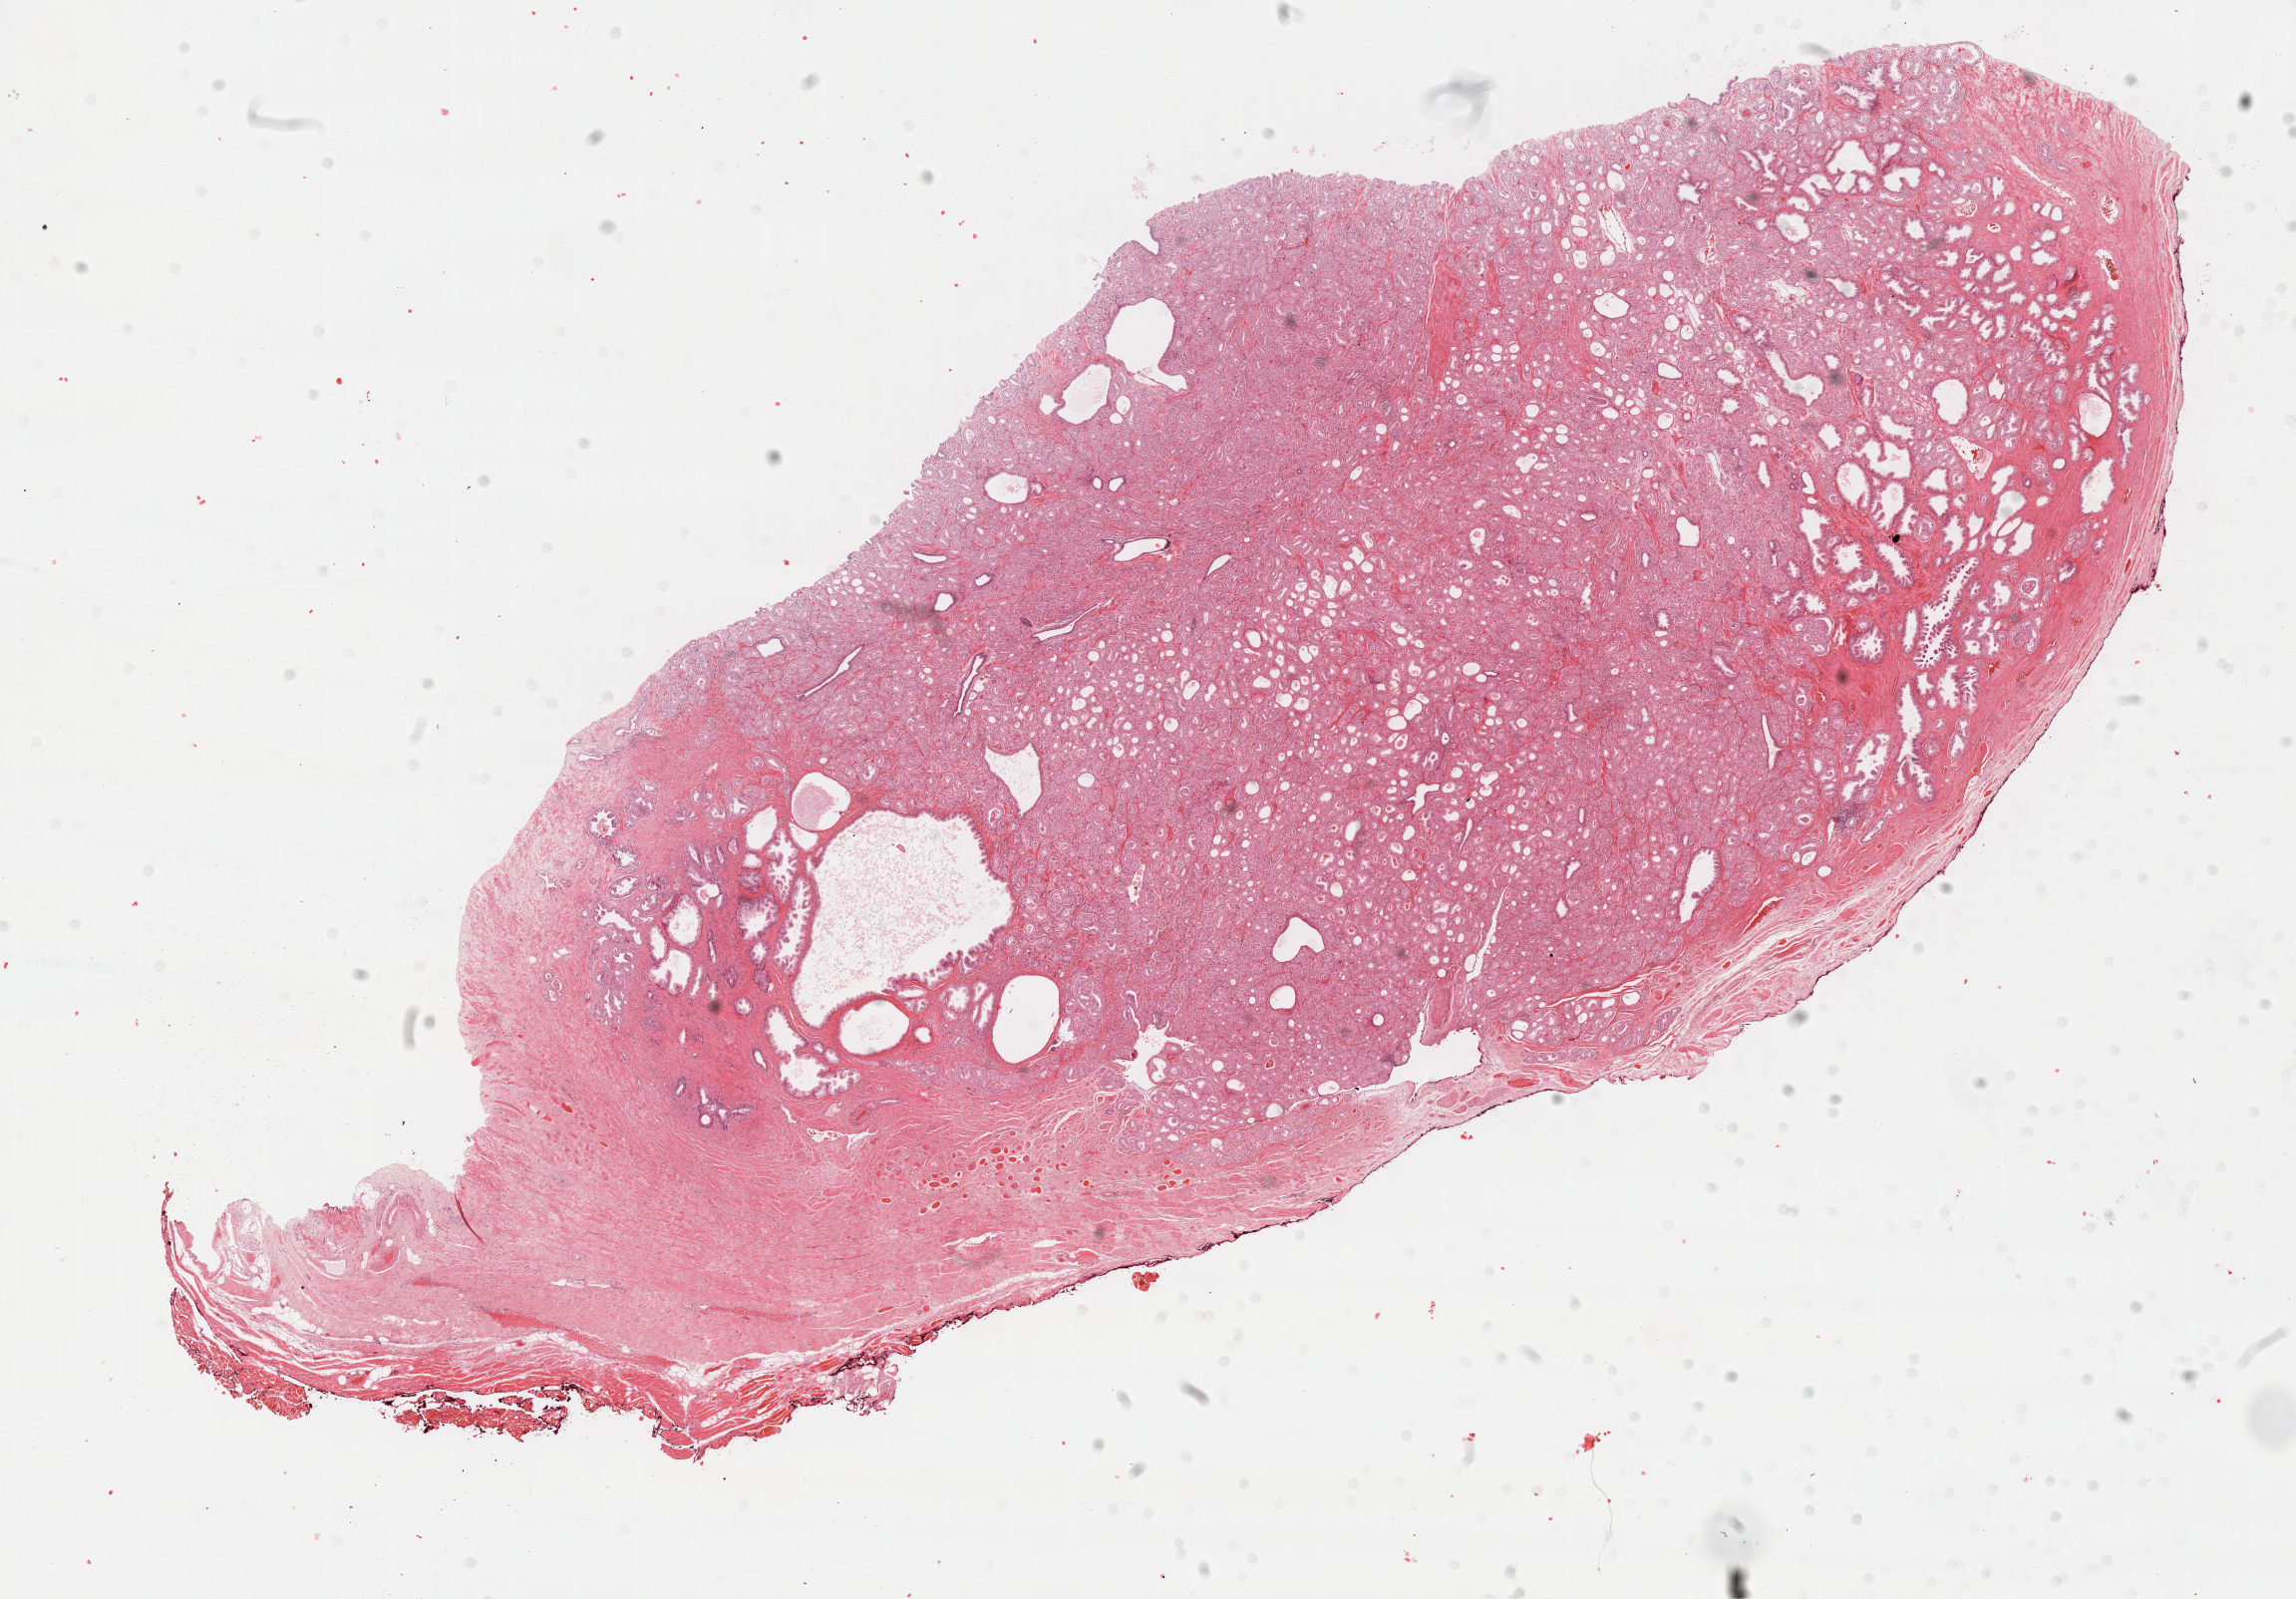
Whole-slide histology image, H&E, a low-resolution overview of the entire scanned area, about 18.6 x 13.0 mm (acquisition: 40x scan). Formalin-fixed paraffin-embedded (FFPE) diagnostic section. Sample: primary tumour, prostate. Patient: male, age at initial diagnosis 65 years.
Diagnosis: Adenocarcinoma, NOS.